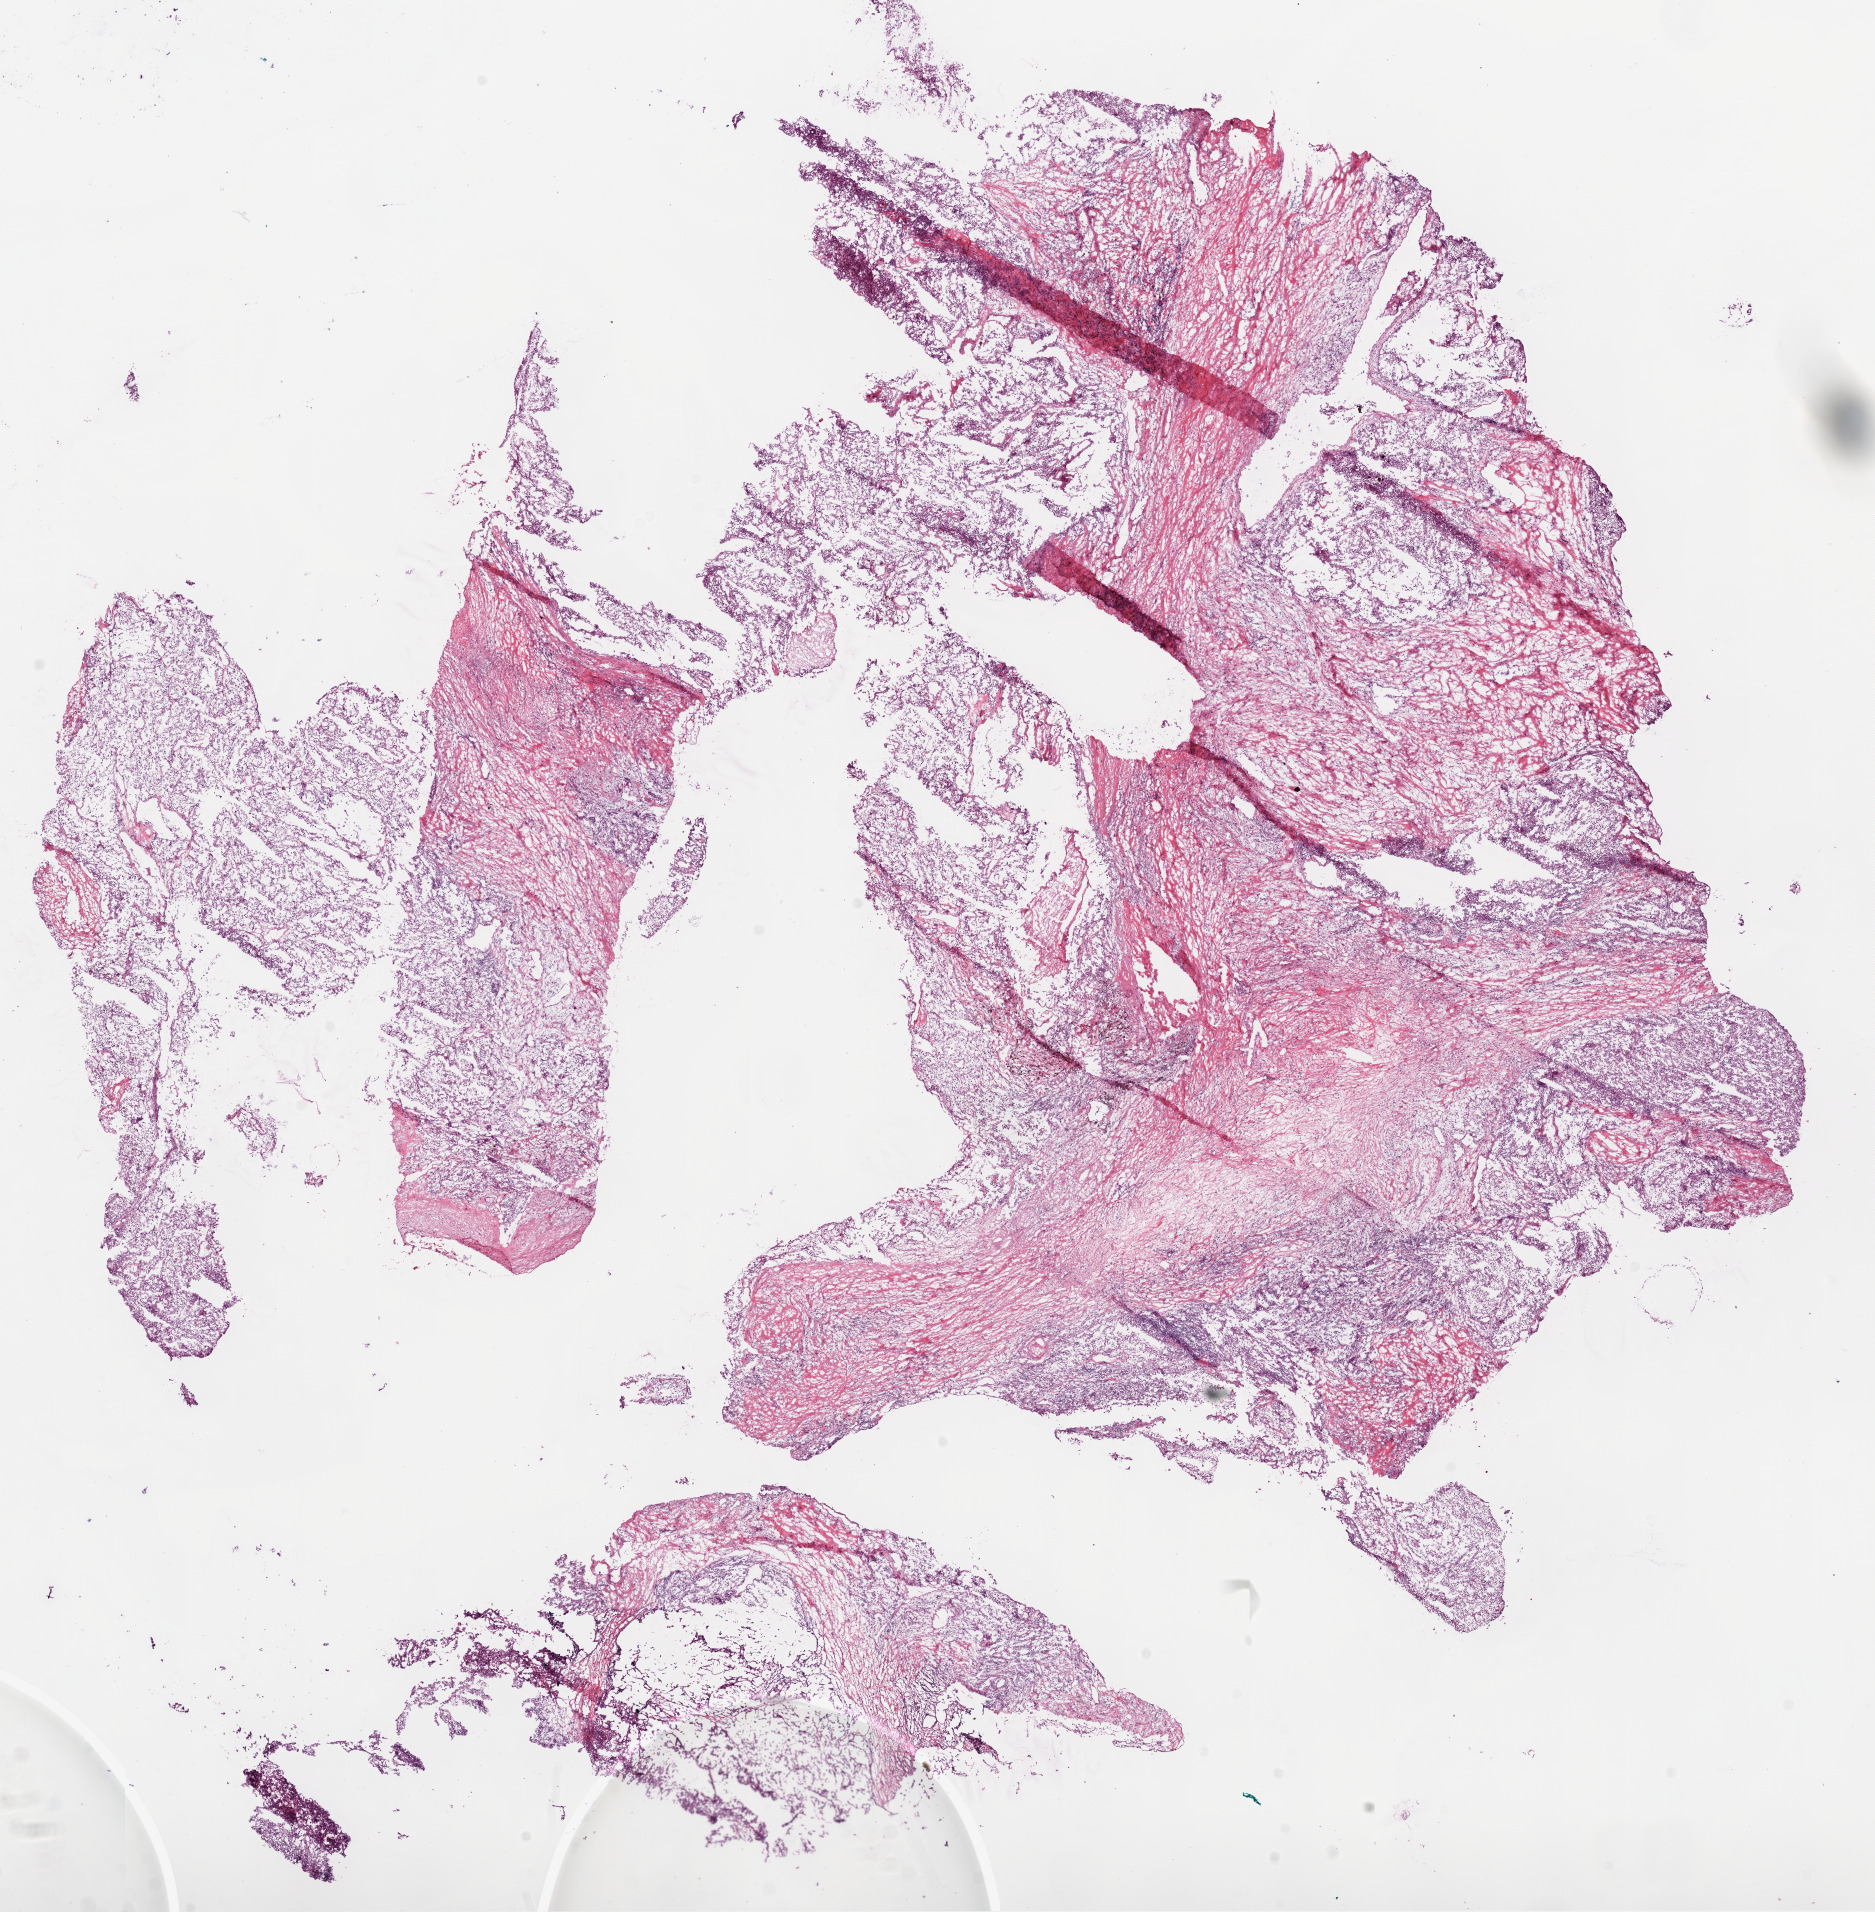
H&E whole-slide image, whole scanned area (about 15.0 x 15.3 mm, from a 20x scan) shown as a low-resolution overview. Frozen section. Primary tumour sample from the kidney. Male patient; age at initial diagnosis 68 years. Histologic grade: G2 (moderately differentiated). Slide review estimates, as recorded: tumour cells 65%, tumour nuclei 70%, normal cells 0%, stromal cells 30%, necrosis 5%. Infiltration values recorded for this section: lymphocyte infiltration 18%, monocyte infiltration 5%, neutrophil infiltration 0%.
* lymph nodes positive (case pathology): 0 of 6 examined
* pathologic diagnosis: Clear cell adenocarcinoma, NOS
* laterality: left
* AJCC pathologic stage: I